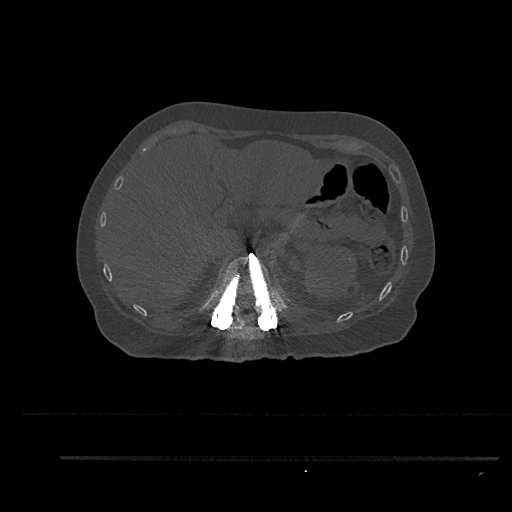
CT including the spine, one axial slice. Reconstruction kernel Br40s/3. 120 kVp. Bone window (W 1800 / L 400 HU). 0.5 mm slice thickness. 512 × 512 image matrix. Female patient, age 44 years. From the clinical record (not read from this slice): primary cancer: renal; vertebrae with lytic lesions (as recorded): L1.
Structures marked on this image (semi-automatic segmentation, software-assisted and operator-edited):
- T11 vertebra: bounding box <232,319,245,330> (left, top, right, bottom; pixels)
- T12 vertebra: <214,255,282,319>